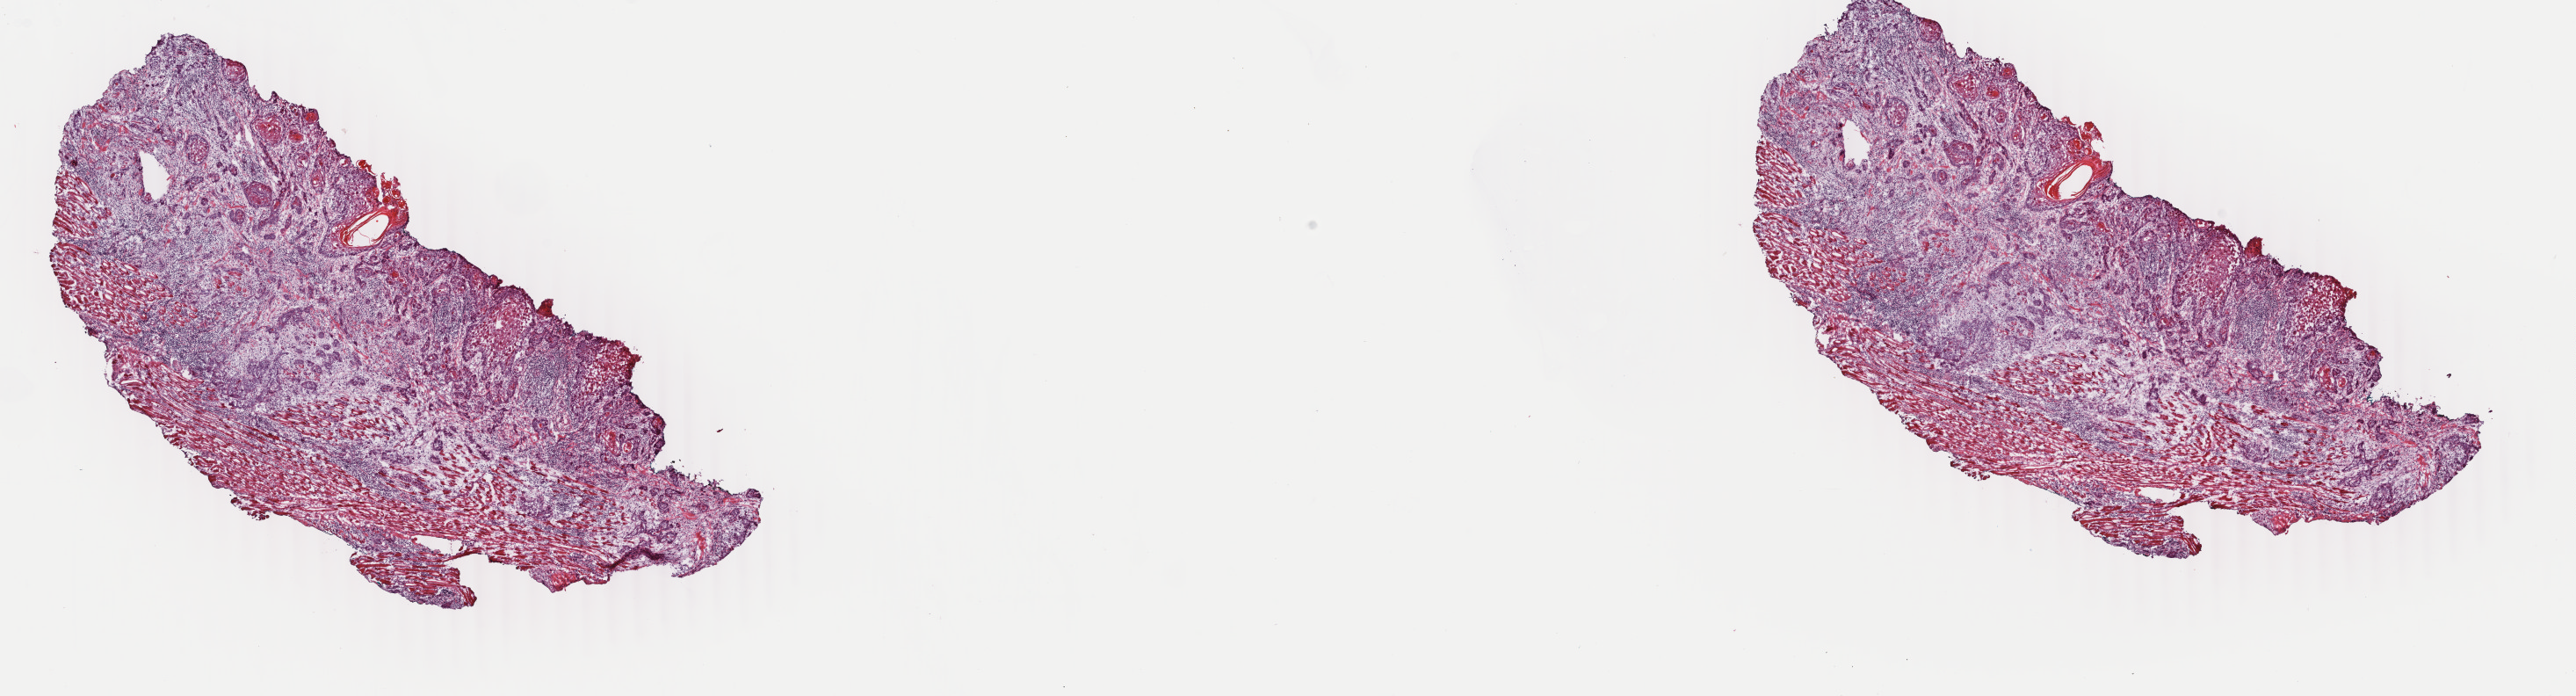
H&E-stained whole-slide image, shown as a low-resolution overview of the whole scanned area (about 23.3 x 6.3 mm, slide scanned at 40x); frozen section from the top of the tissue portion; head and neck, primary tumour sample. Male patient; age at initial diagnosis 60 years. Histologic grade: G2 (moderately differentiated). Composition of this section per pathologist review: tumour cells 60%, tumour nuclei 70%, normal cells 10%, stromal cells 30%, necrosis 0%. Infiltration values recorded for this section: lymphocyte infiltration 10%, monocyte infiltration 0%, neutrophil infiltration 0%.
• TNM: T1 N1 MX
• histologic diagnosis: Squamous cell carcinoma, NOS
• laterality: left
• AJCC pathologic stage: III